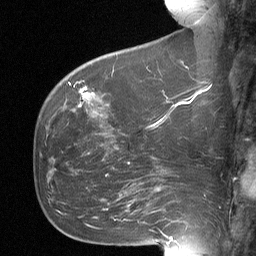
Breast MRI (dynamic contrast-enhanced), one sagittal slice; position 18 of 64 along the scan axis; dynamic contrast-enhanced study with each time point stored as its own series, time point 2 of 3 at this slice position (early post-contrast, ordered by acquisition time); 1.5 T; TE 4.8 ms, TR 27 ms; 256 × 256 image matrix, field of view 200 × 200 mm. Patient: female, 60 years. Case-level facts recorded for this patient, not image findings: setting: breast cancer imaged before/during neoadjuvant chemotherapy; receptor status: HR-positive, HER2-negative.
Structures marked on this image (semi-automatically segmented with operator editing):
- analysis volume of interest (the breast-tissue region the enhancement analysis was run in; not a lesion): bounding box <67,68,109,112> (left, top, right, bottom; pixels)
- tumour enhancement mask (voxels above the 90 % enhancement threshold inside the analysis volume of interest): <81,87,88,97>